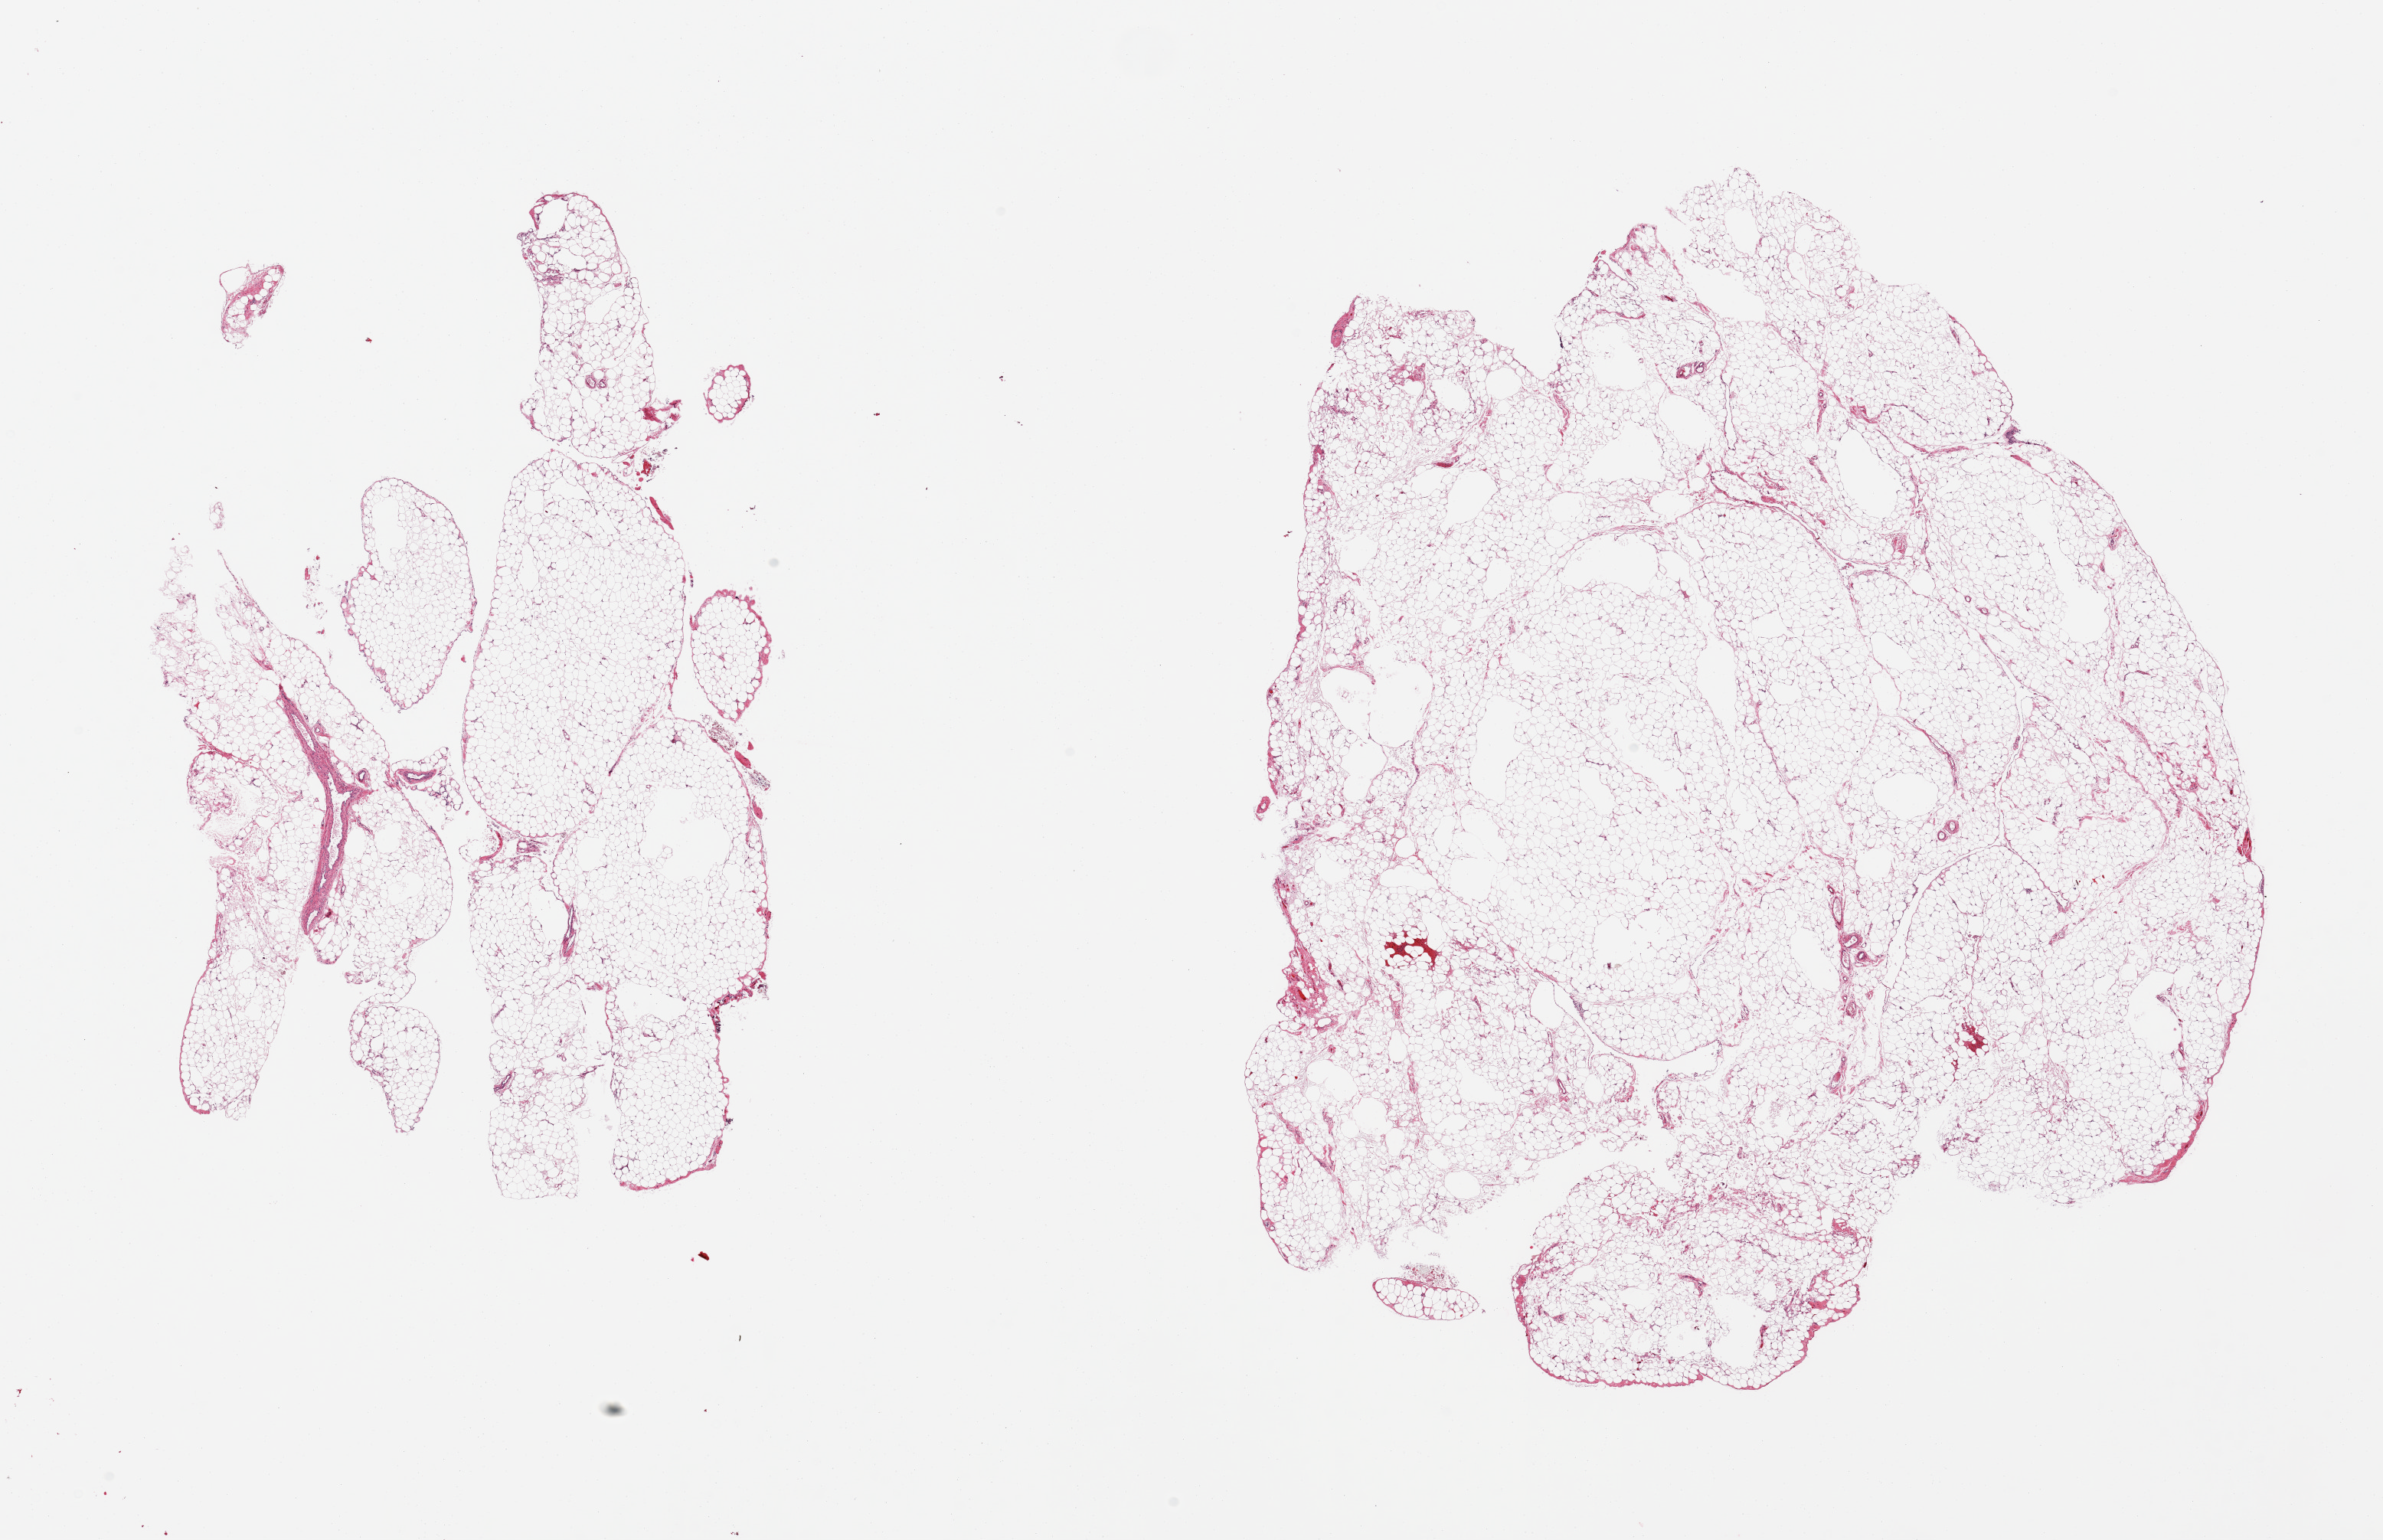
Digitized hematoxylin and eosin (H&E)-stained section — low-resolution overview of the scanned area, about 24.6 x 15.9 mm, PAXgene-fixed paraffin-embedded (PFPE) section, section of omentum (target tissue), donor tissue sample. Donor sex: female.
Pathologist's review note for this sample: 2 pieces, only trace fascia/vascular elements.